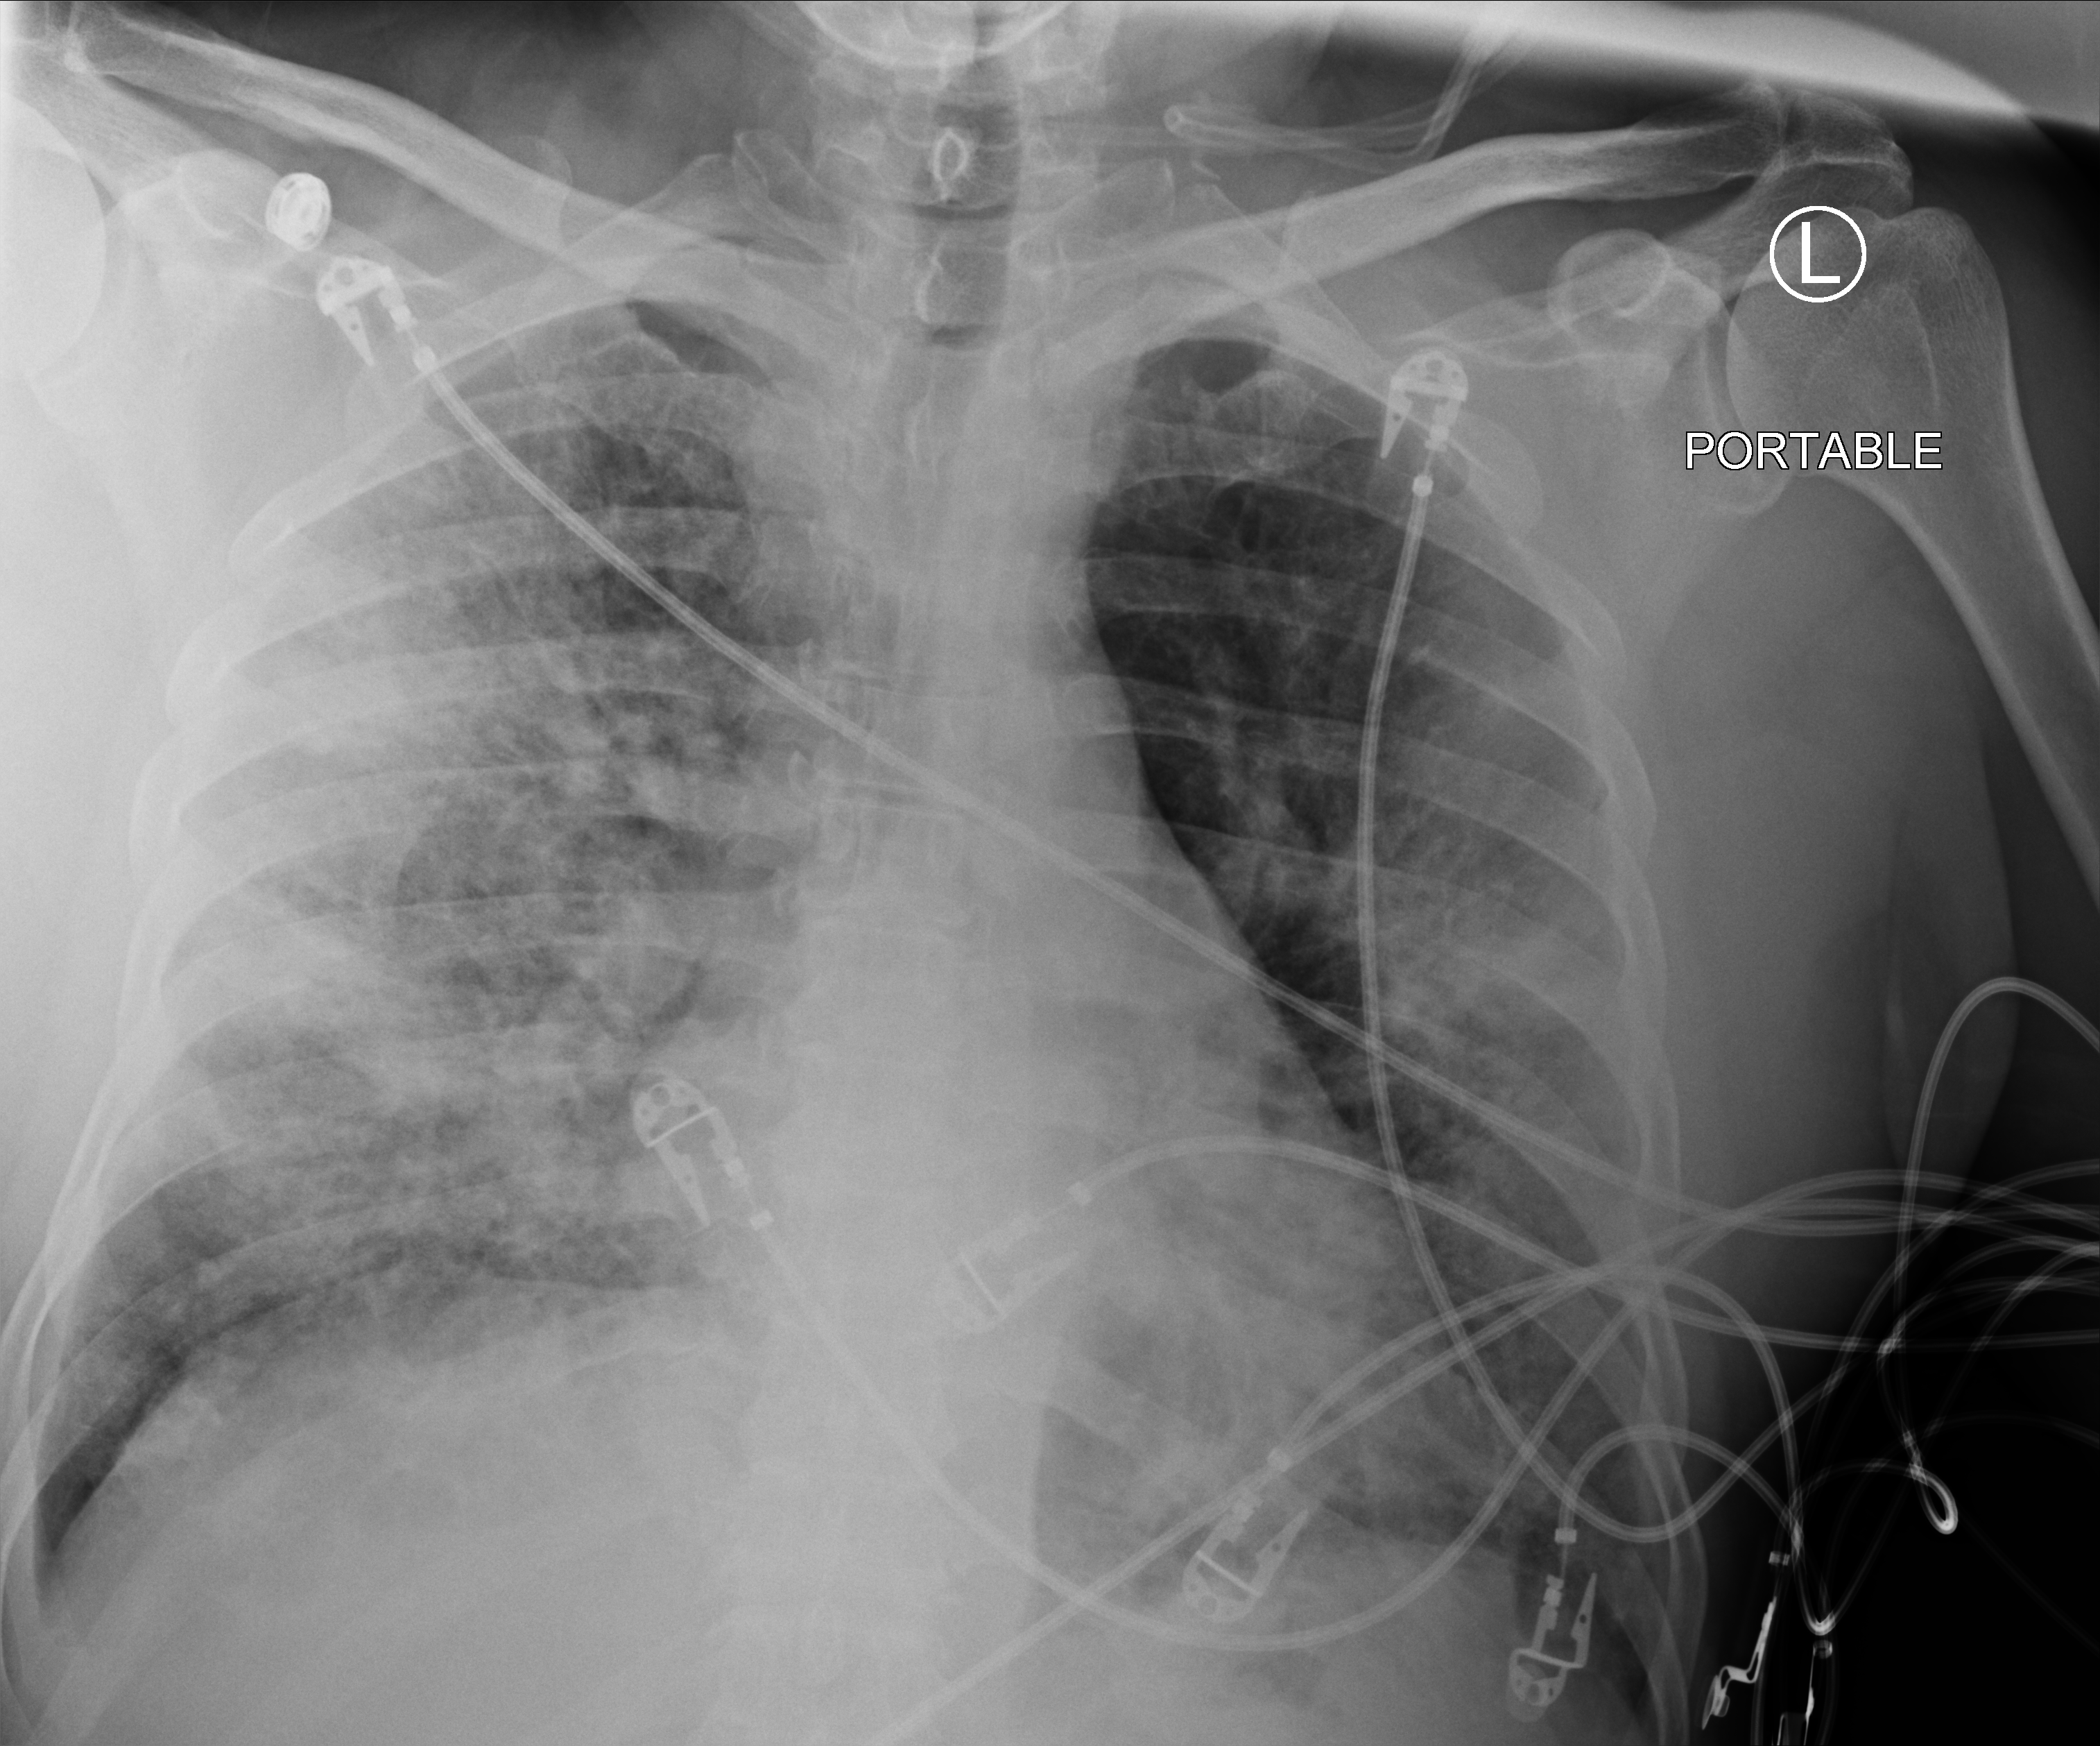
Portable chest radiograph, anteroposterior (AP) projection. Male patient hospitalised with COVID-19, age 18–59 years.
Hospital-stay facts (about this admission, not read from this image; timing relative to this image not recorded): mechanically ventilated during this hospital stay: no; chronic kidney disease (admission record): no.